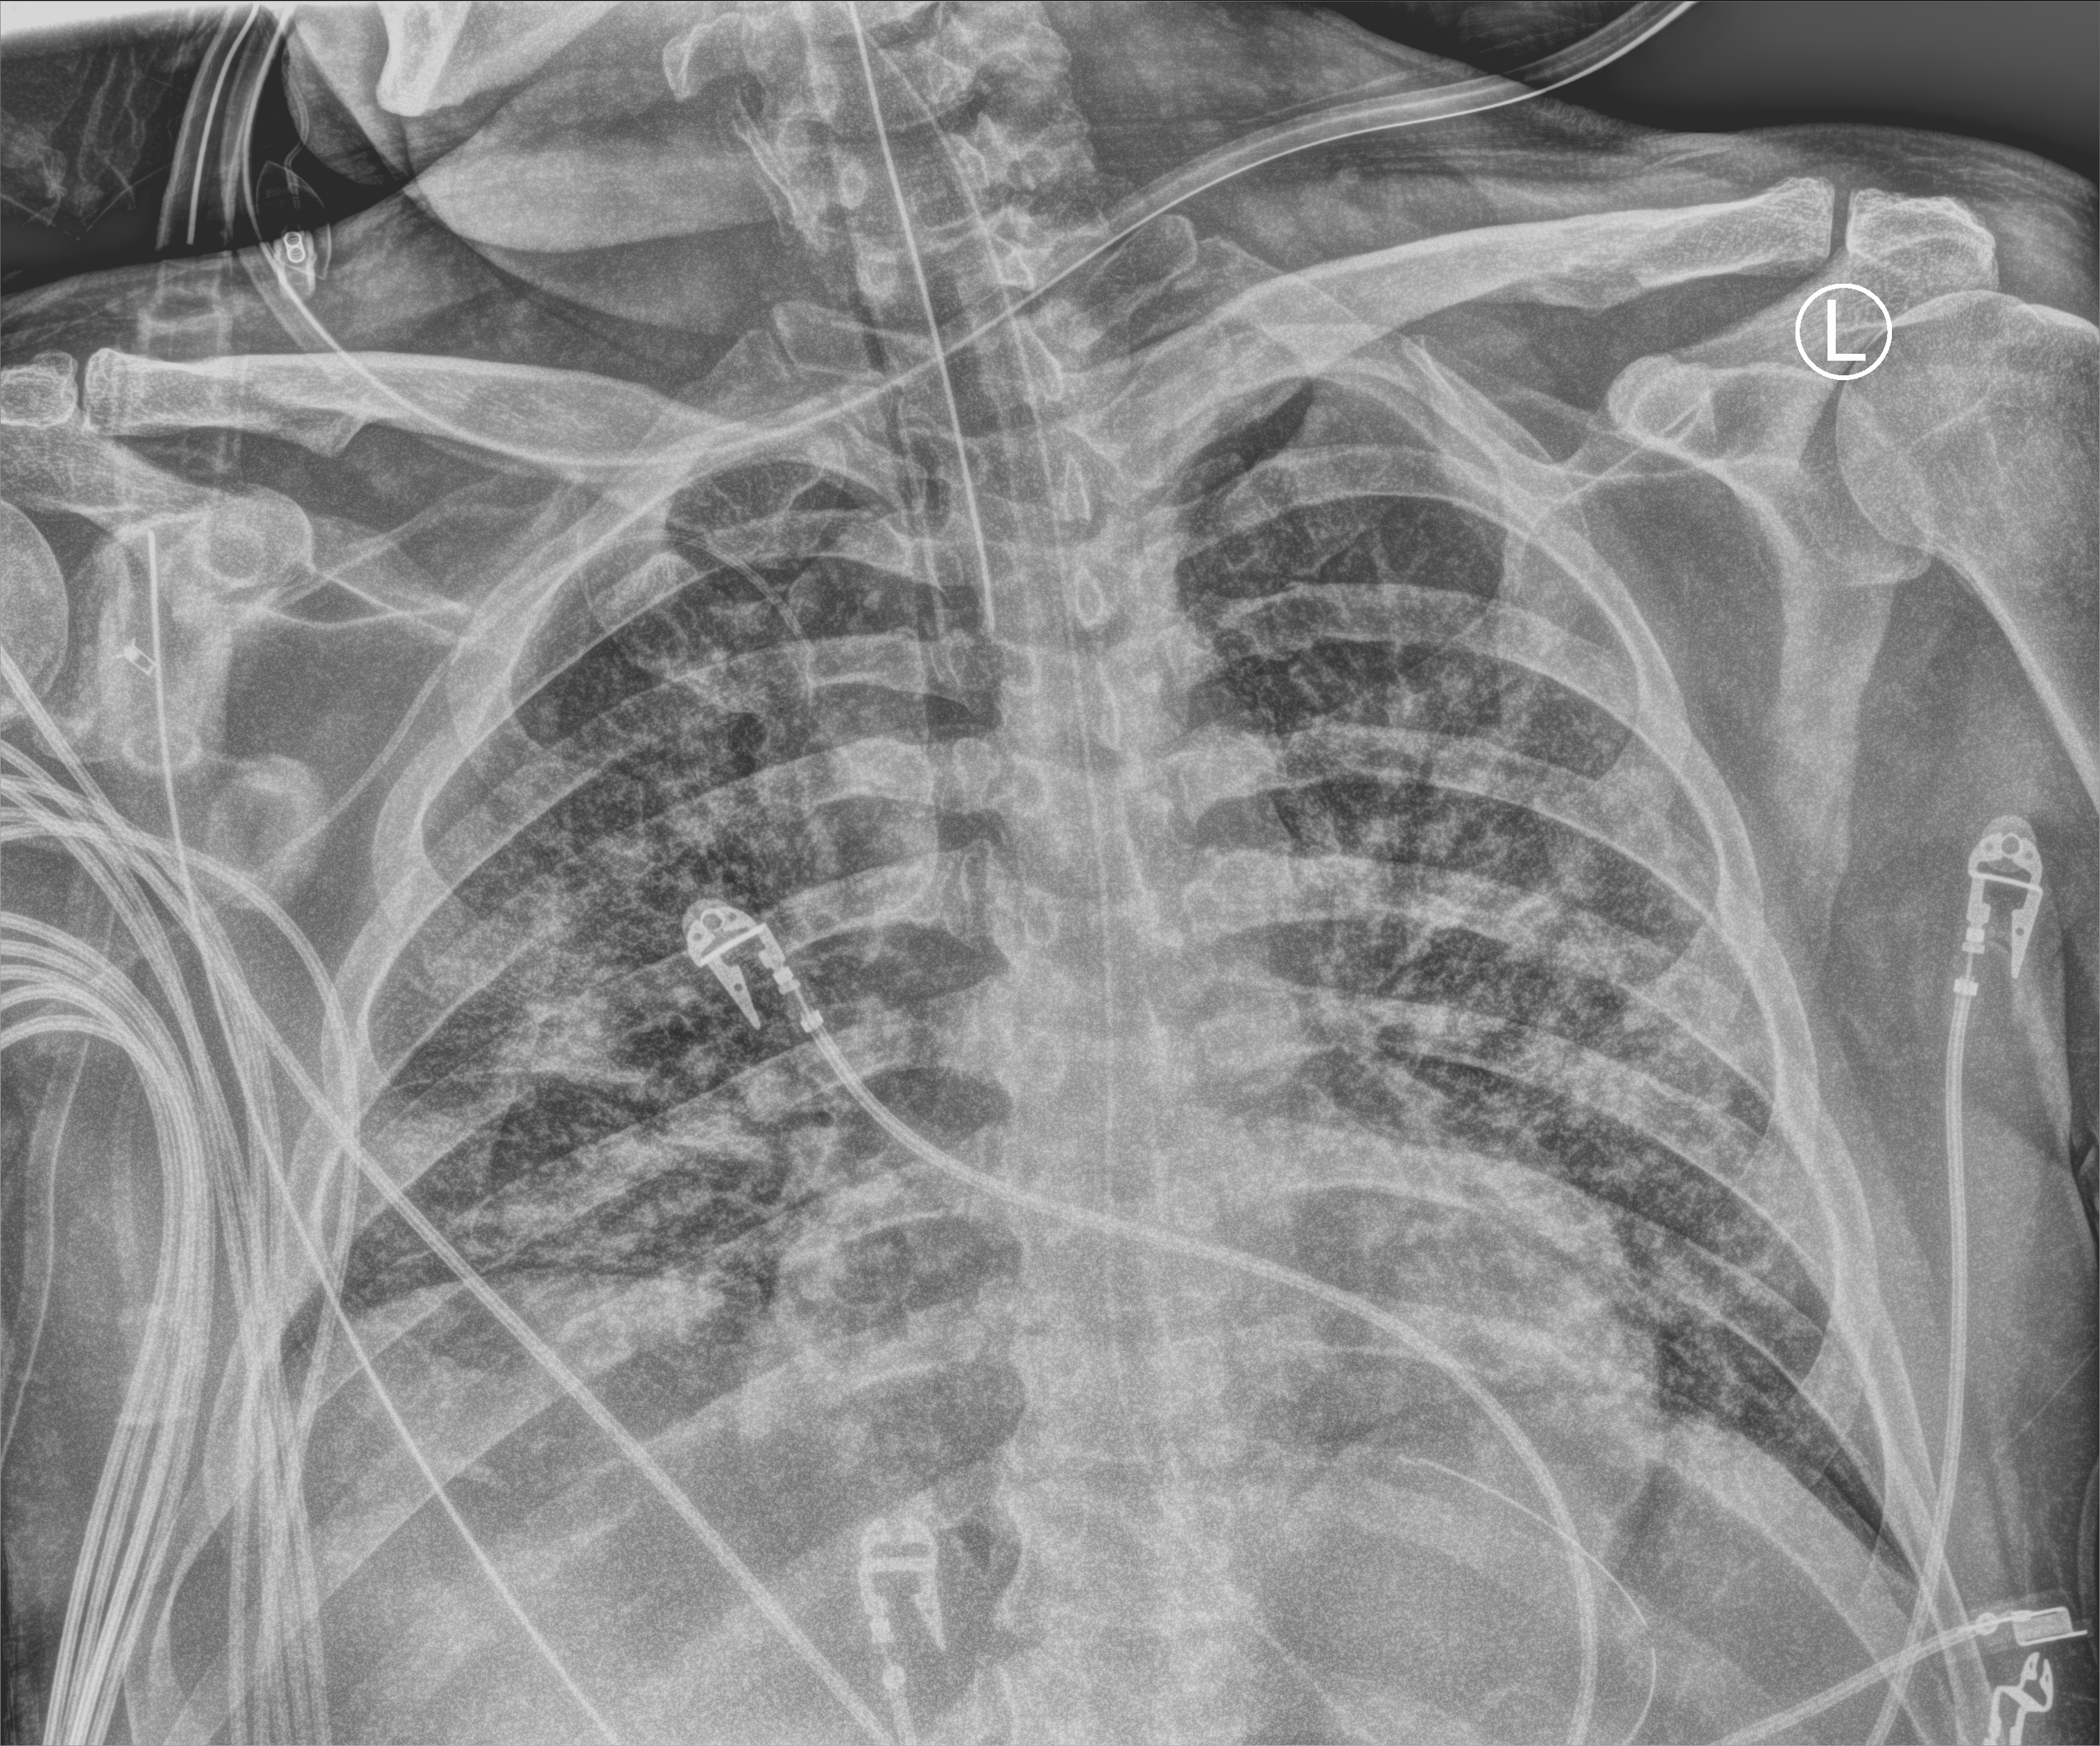
Chest X-ray (portable), anteroposterior (AP) projection. Patient hospitalised with COVID-19; male, aged 18–59 years.
From the hospital-stay record, not from the radiograph (when in the stay this image was taken is not recorded):
- admitted to intensive care during this hospital stay: yes